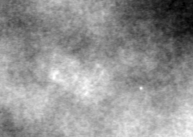
Cropped region of a digitized screen-film mammogram centred on a radiologist-marked abnormality; left breast; CC view; BI-RADS breast density category 4 (scale 1–4).
Calcifications, morphology pleomorphic, distribution clustered; BI-RADS assessment category 4; pathology (as recorded): benign.